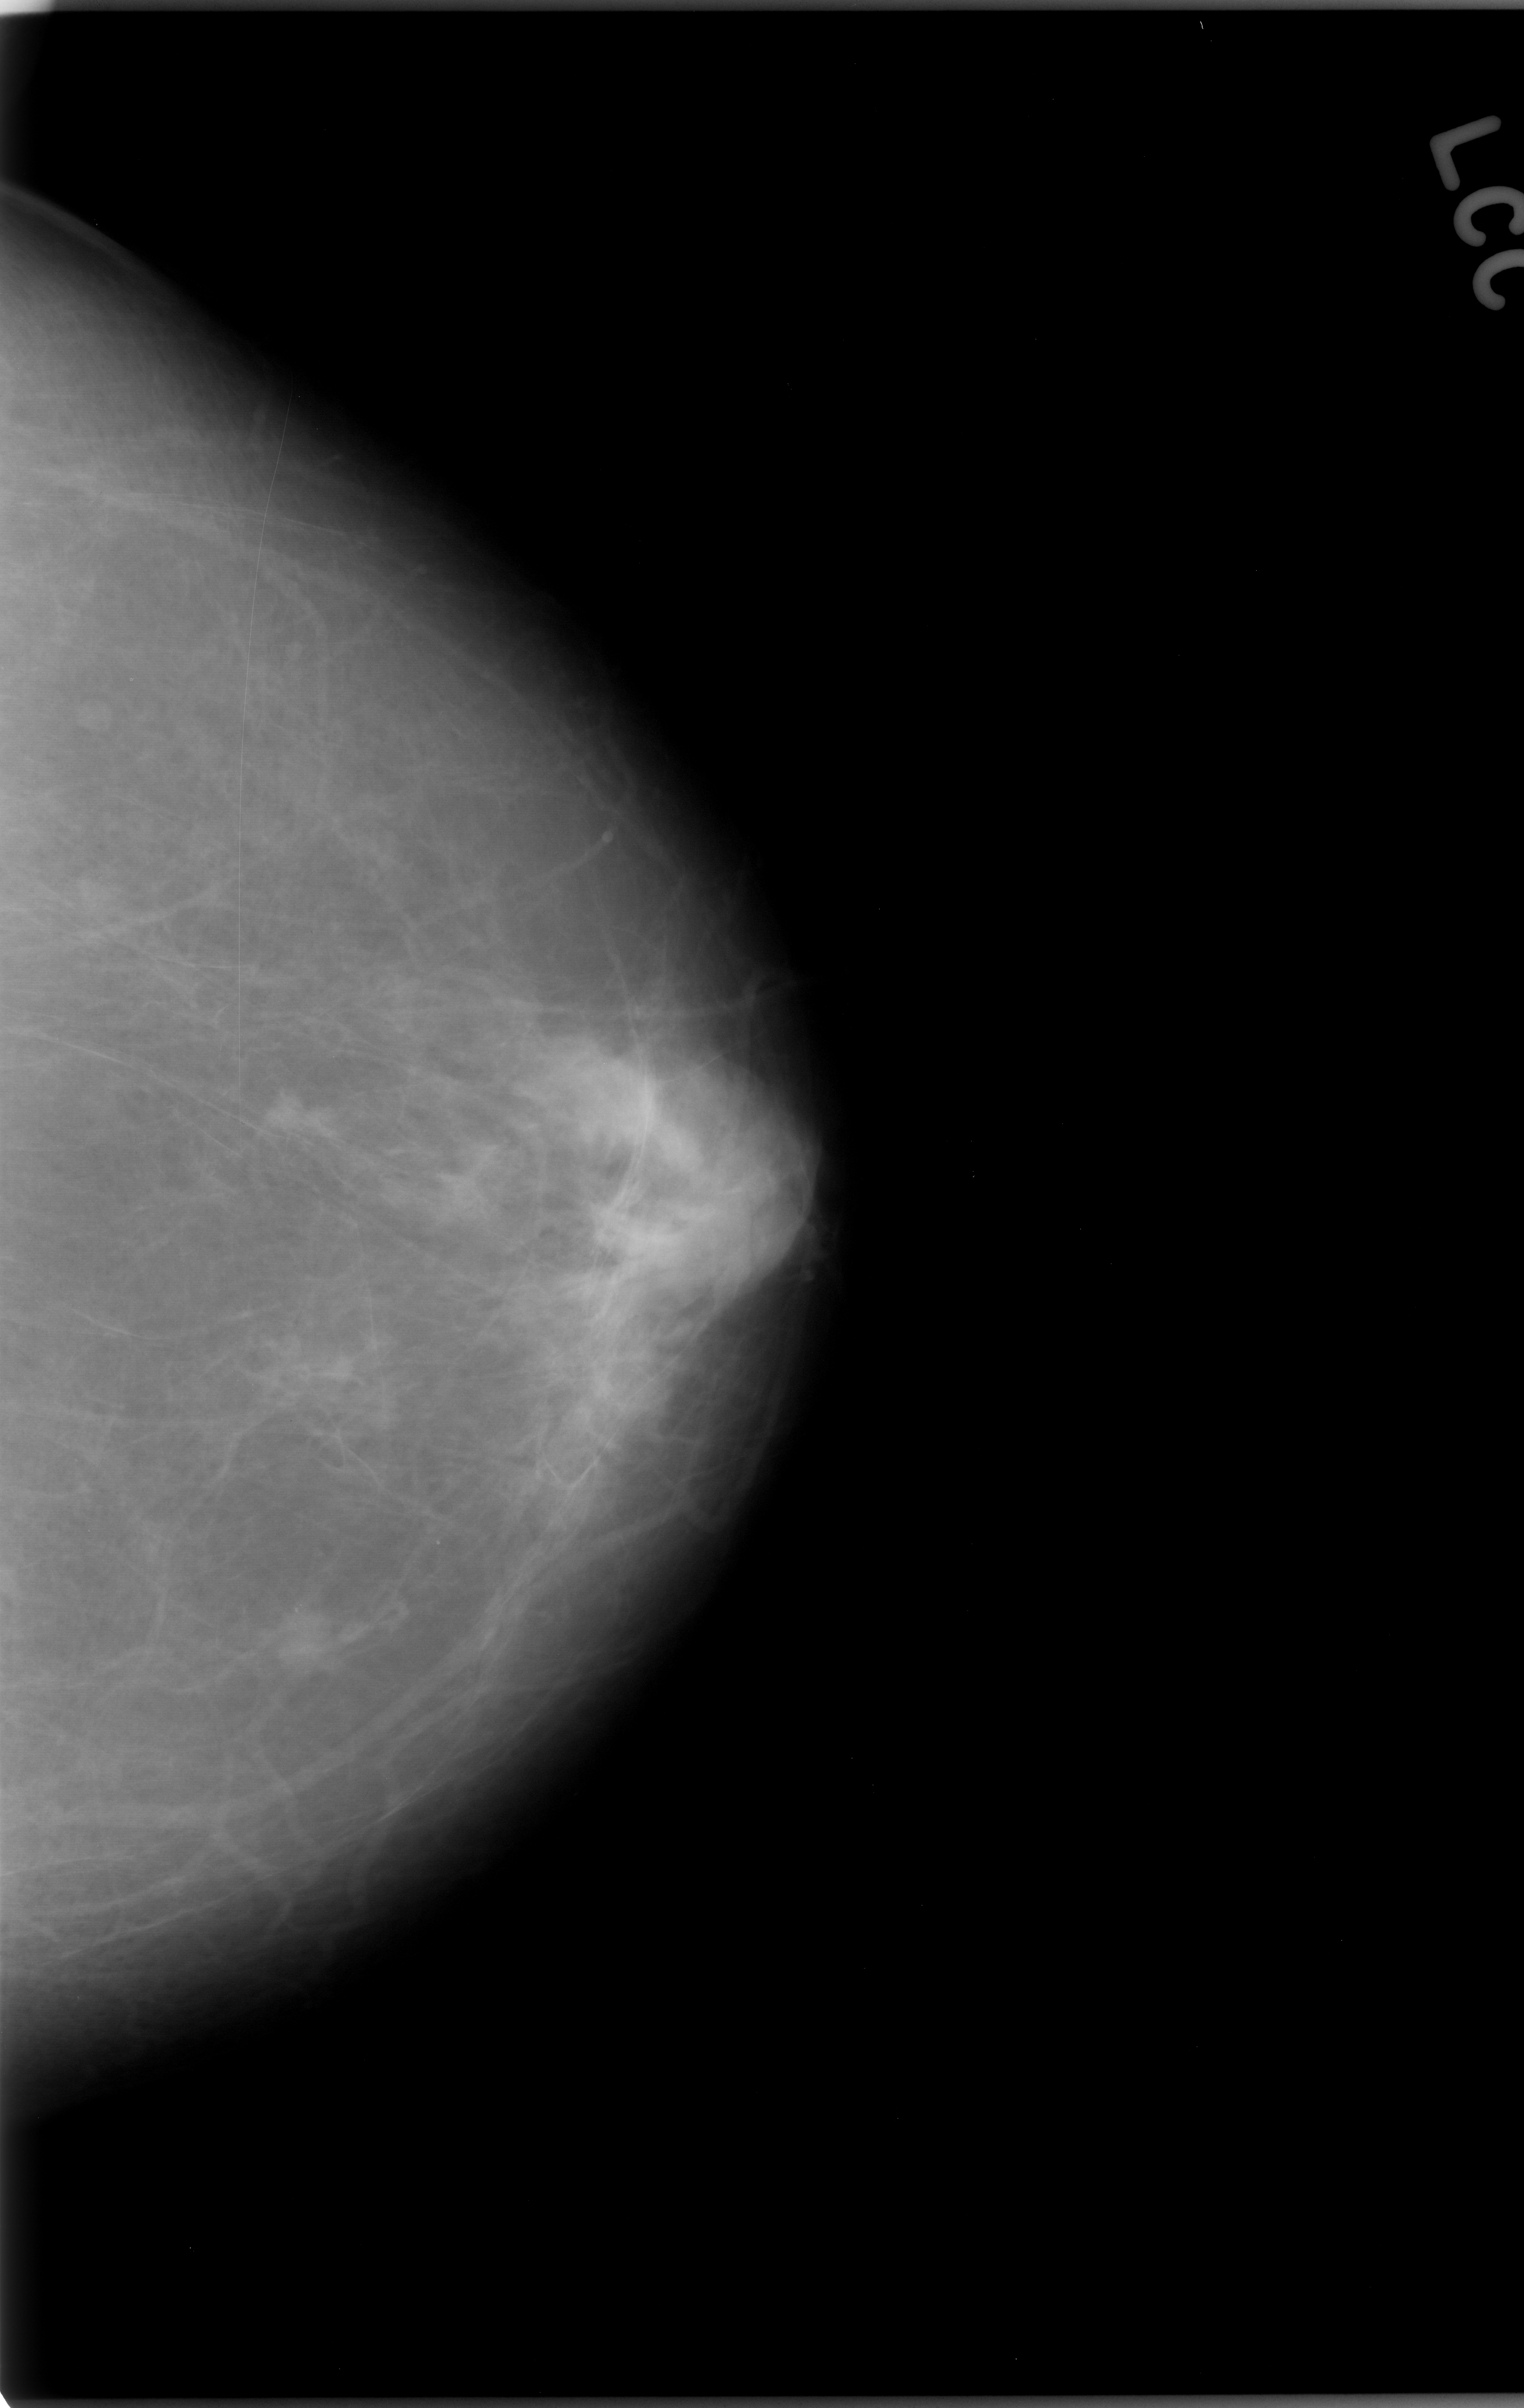
Scanned film-screen mammogram; left breast; craniocaudal (CC) view; breast composition: almost entirely fatty (BI-RADS density category 1 of 4).
Marked abnormality: mass, shape lobulated, margins microlobulated; BI-RADS assessment category 5; subtlety rating 4 on a 1 (subtle) to 5 (obvious) scale; pathology (as recorded): malignant.